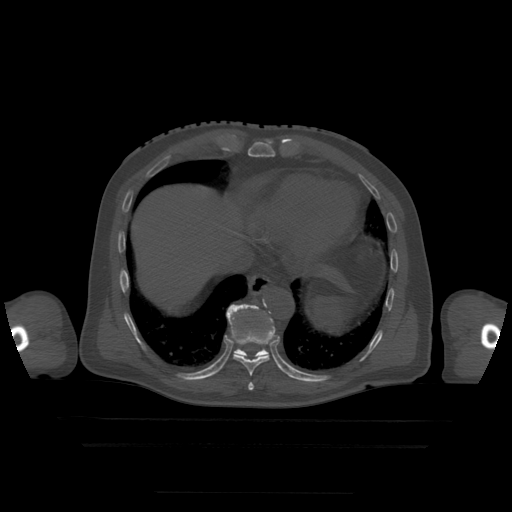
CT including the spine, one axial slice. Position 255 of 522 along the scan axis. Bone window (W 1800 / L 400 HU). 1.25 mm slice thickness. 512 × 512 image matrix. Patient age 68 years. Case-level facts recorded for this patient, not image findings: primary cancer: urothelial.
Annotated regions visible in this slice (semi-automatically segmented with operator editing):
- T10 vertebra: bounding box (x1, y1, x2, y2) in pixels: (226, 304, 269, 357)
- T8 vertebra: (249, 383, 254, 390)
- T9 vertebra: (229, 307, 276, 388)